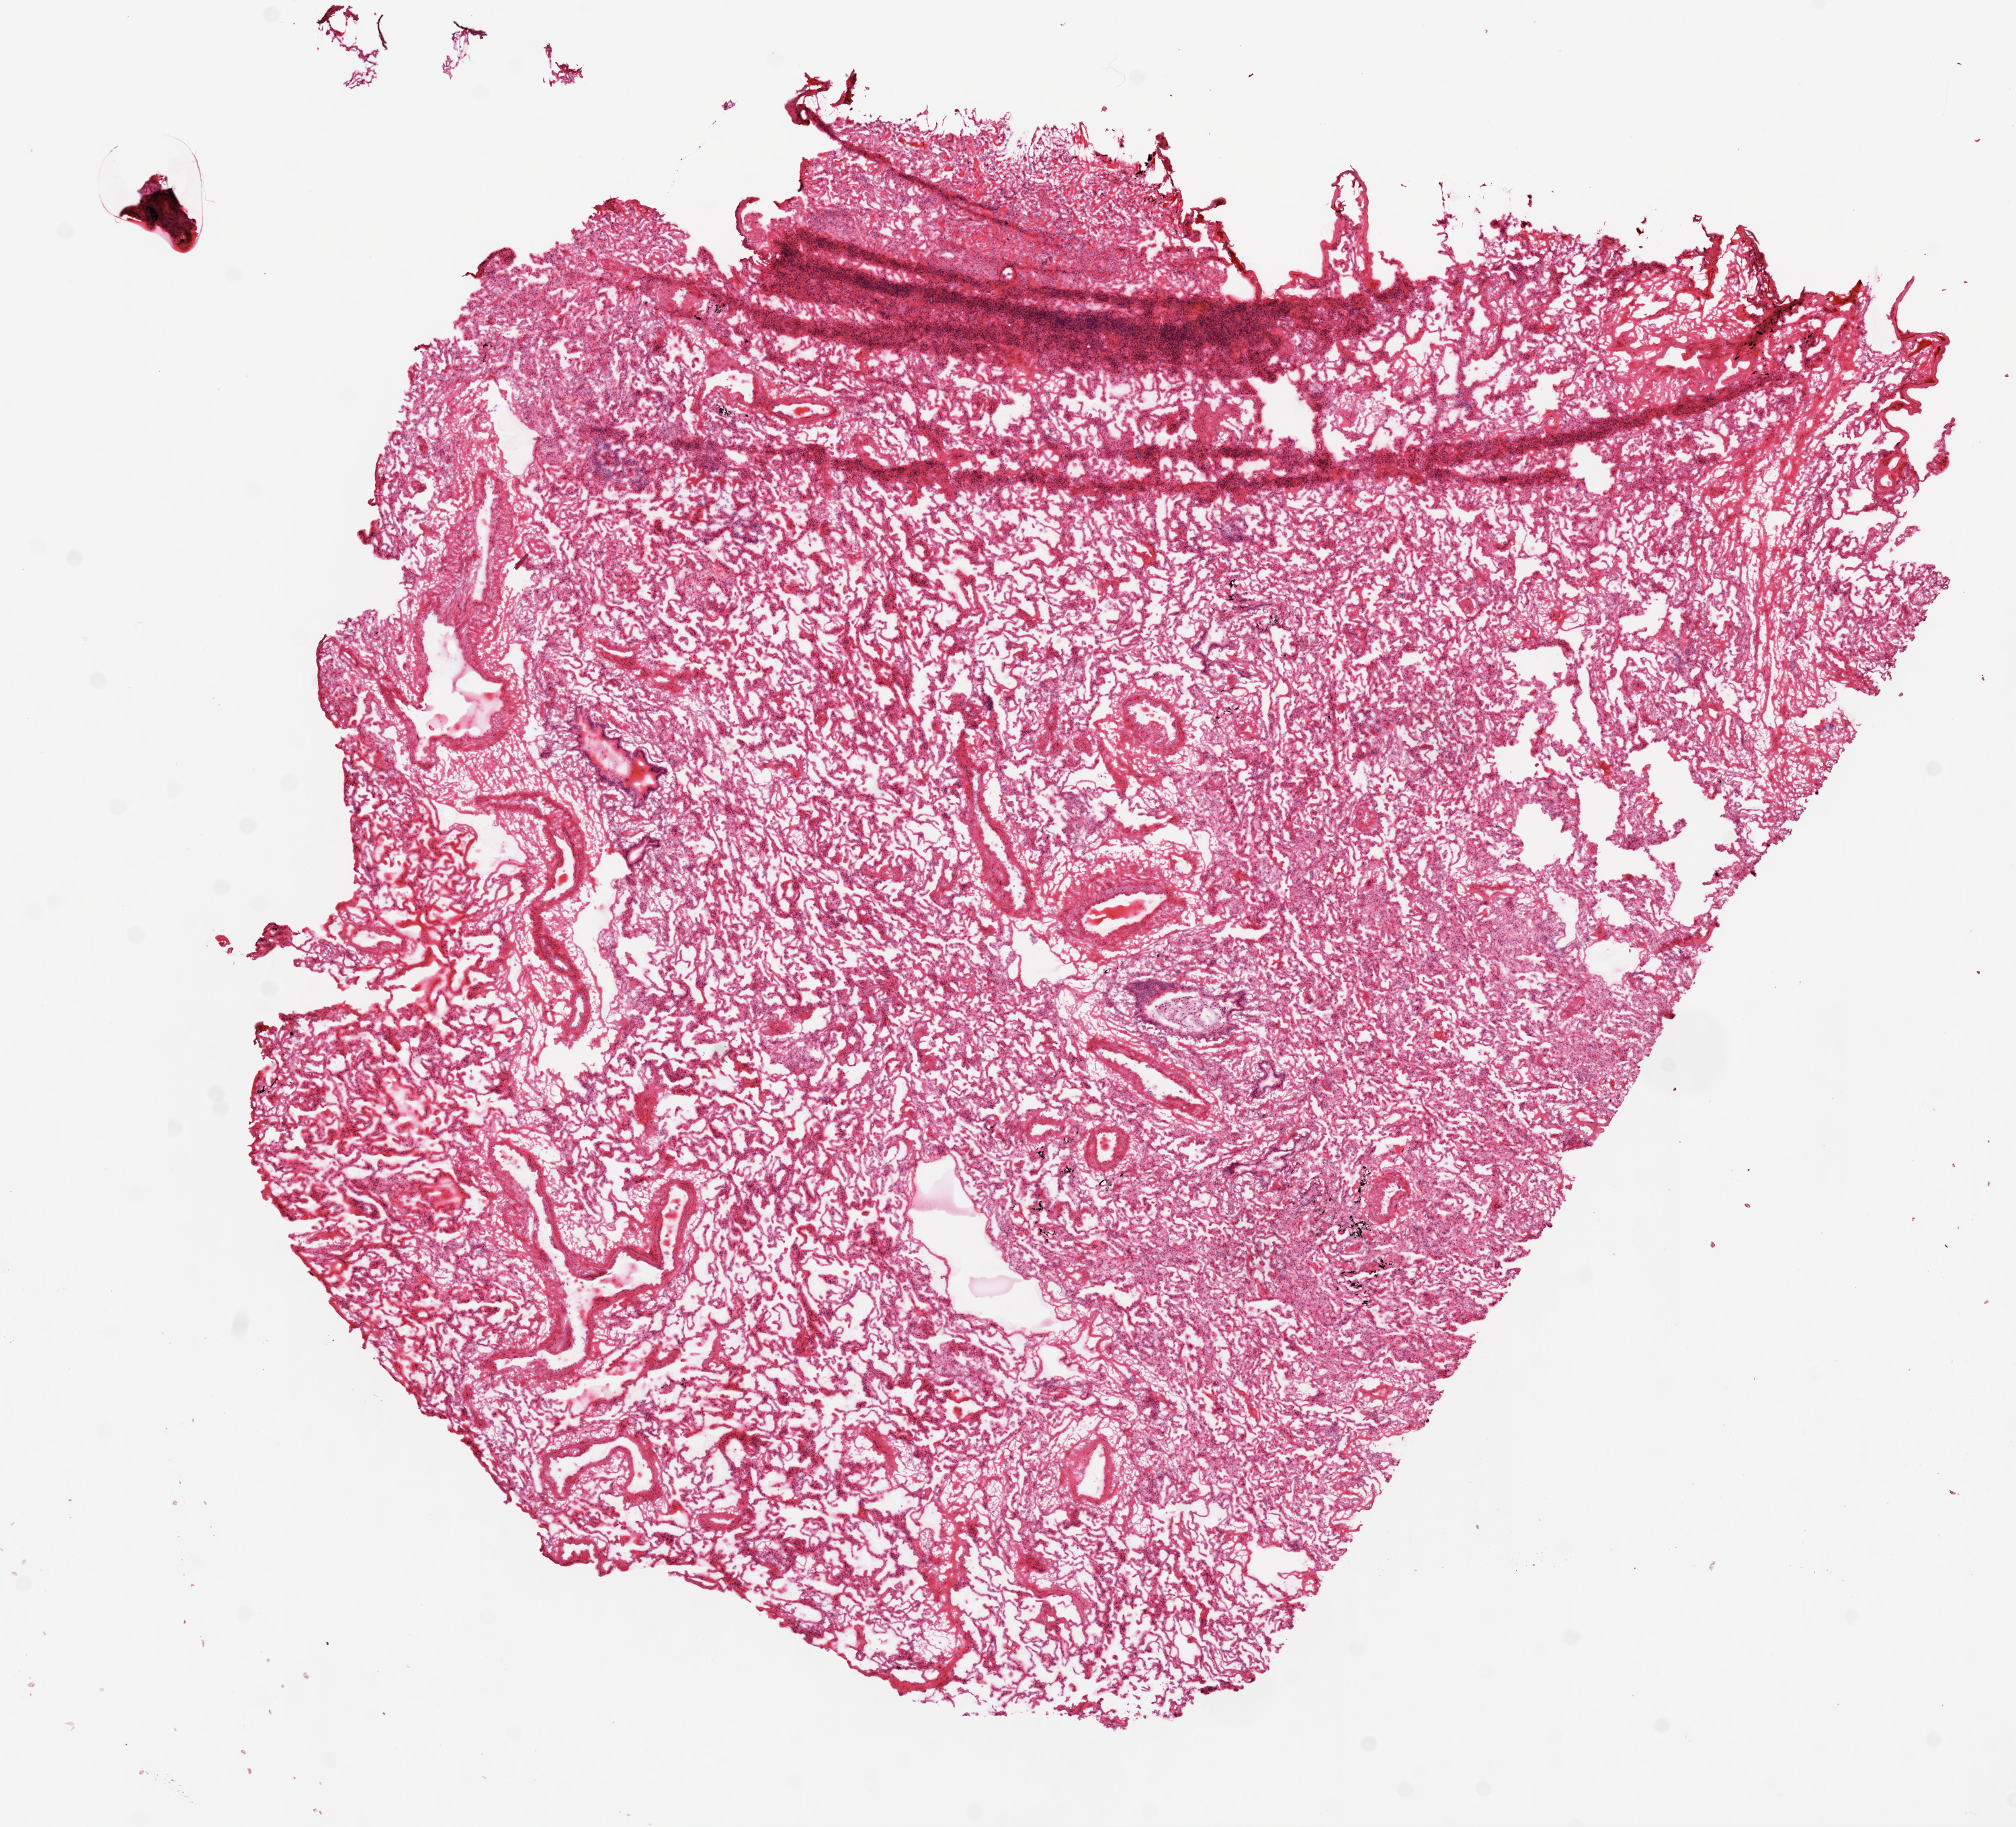
Digitized Hematoxylin and eosin (H&E) stained tissue section (whole slide) — whole scanned area (about 12.0 x 10.9 mm, from a 20x scan) shown as a low-resolution overview; frozen section from the top of the tissue portion; solid tissue normal (non-tumour tissue) sample from the lung. Male, age 81 years at initial diagnosis.
This section: solid tissue normal (non-tumour) sample from the same patient. Patient diagnosis: Squamous cell carcinoma, NOS (upper lobe, lung).